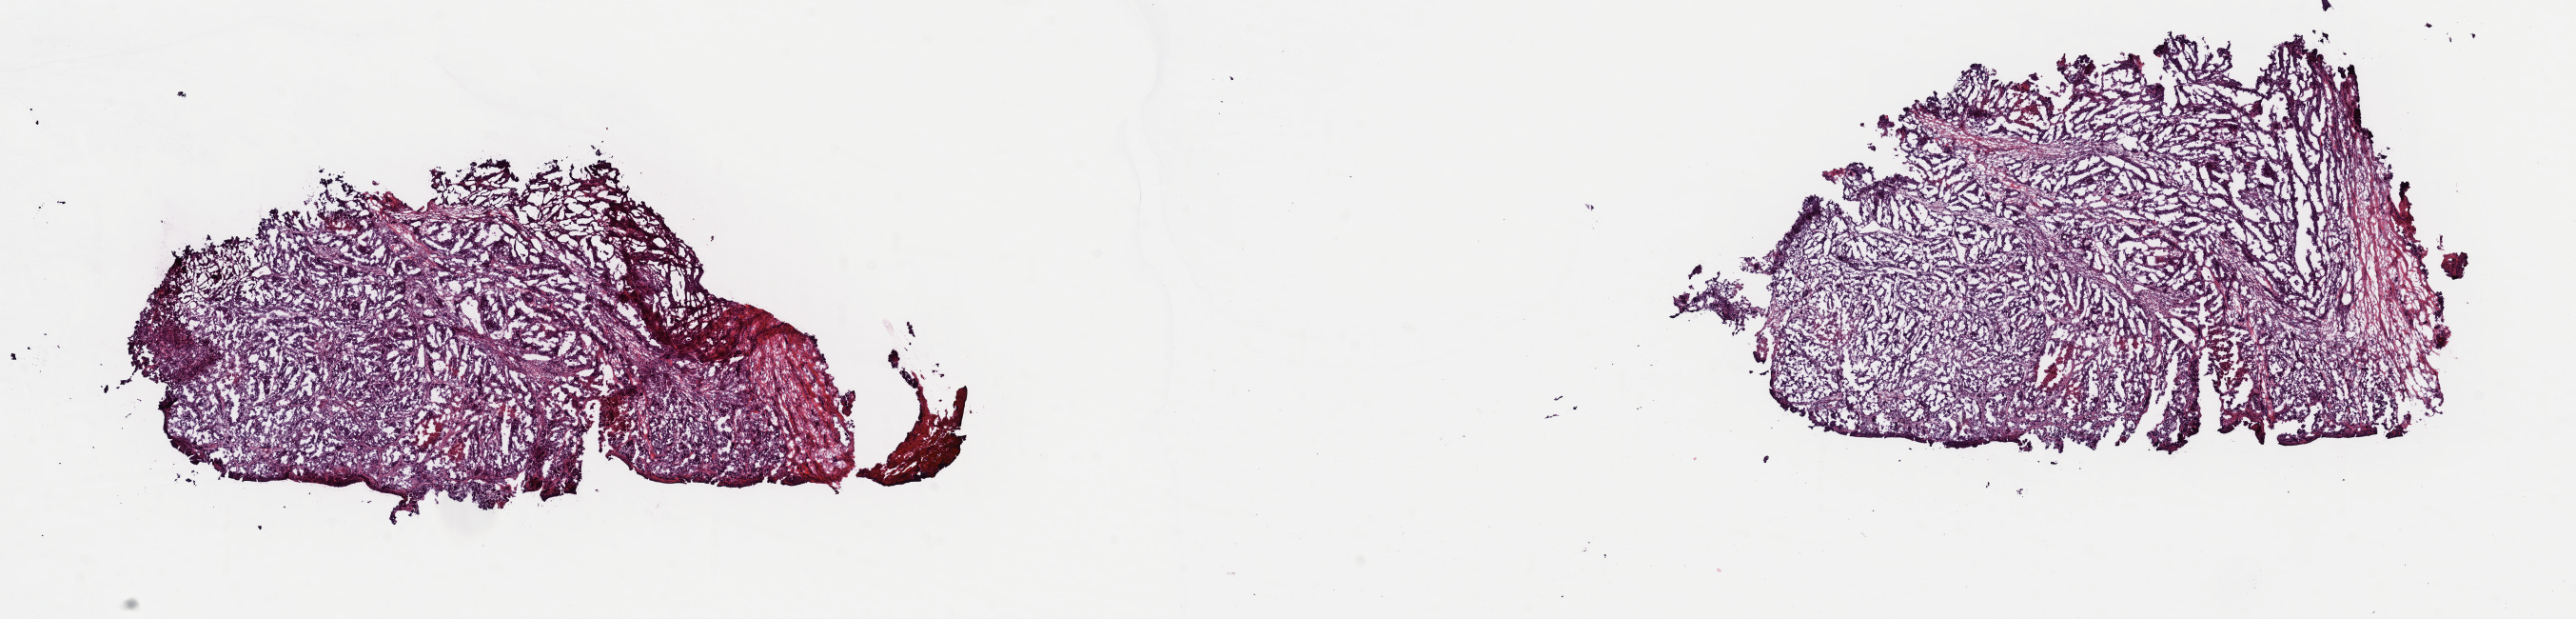
H&E whole-slide image — low-resolution overview of the scanned area, about 21.4 x 5.1 mm (acquisition: 40x scan), frozen section from the top of the tissue portion, metastatic tumour sample, sampled site not recorded. Patient: female, age at initial diagnosis 15 years.
This section: metastatic tumour tissue. Patient diagnosis: Malignant melanoma, NOS.